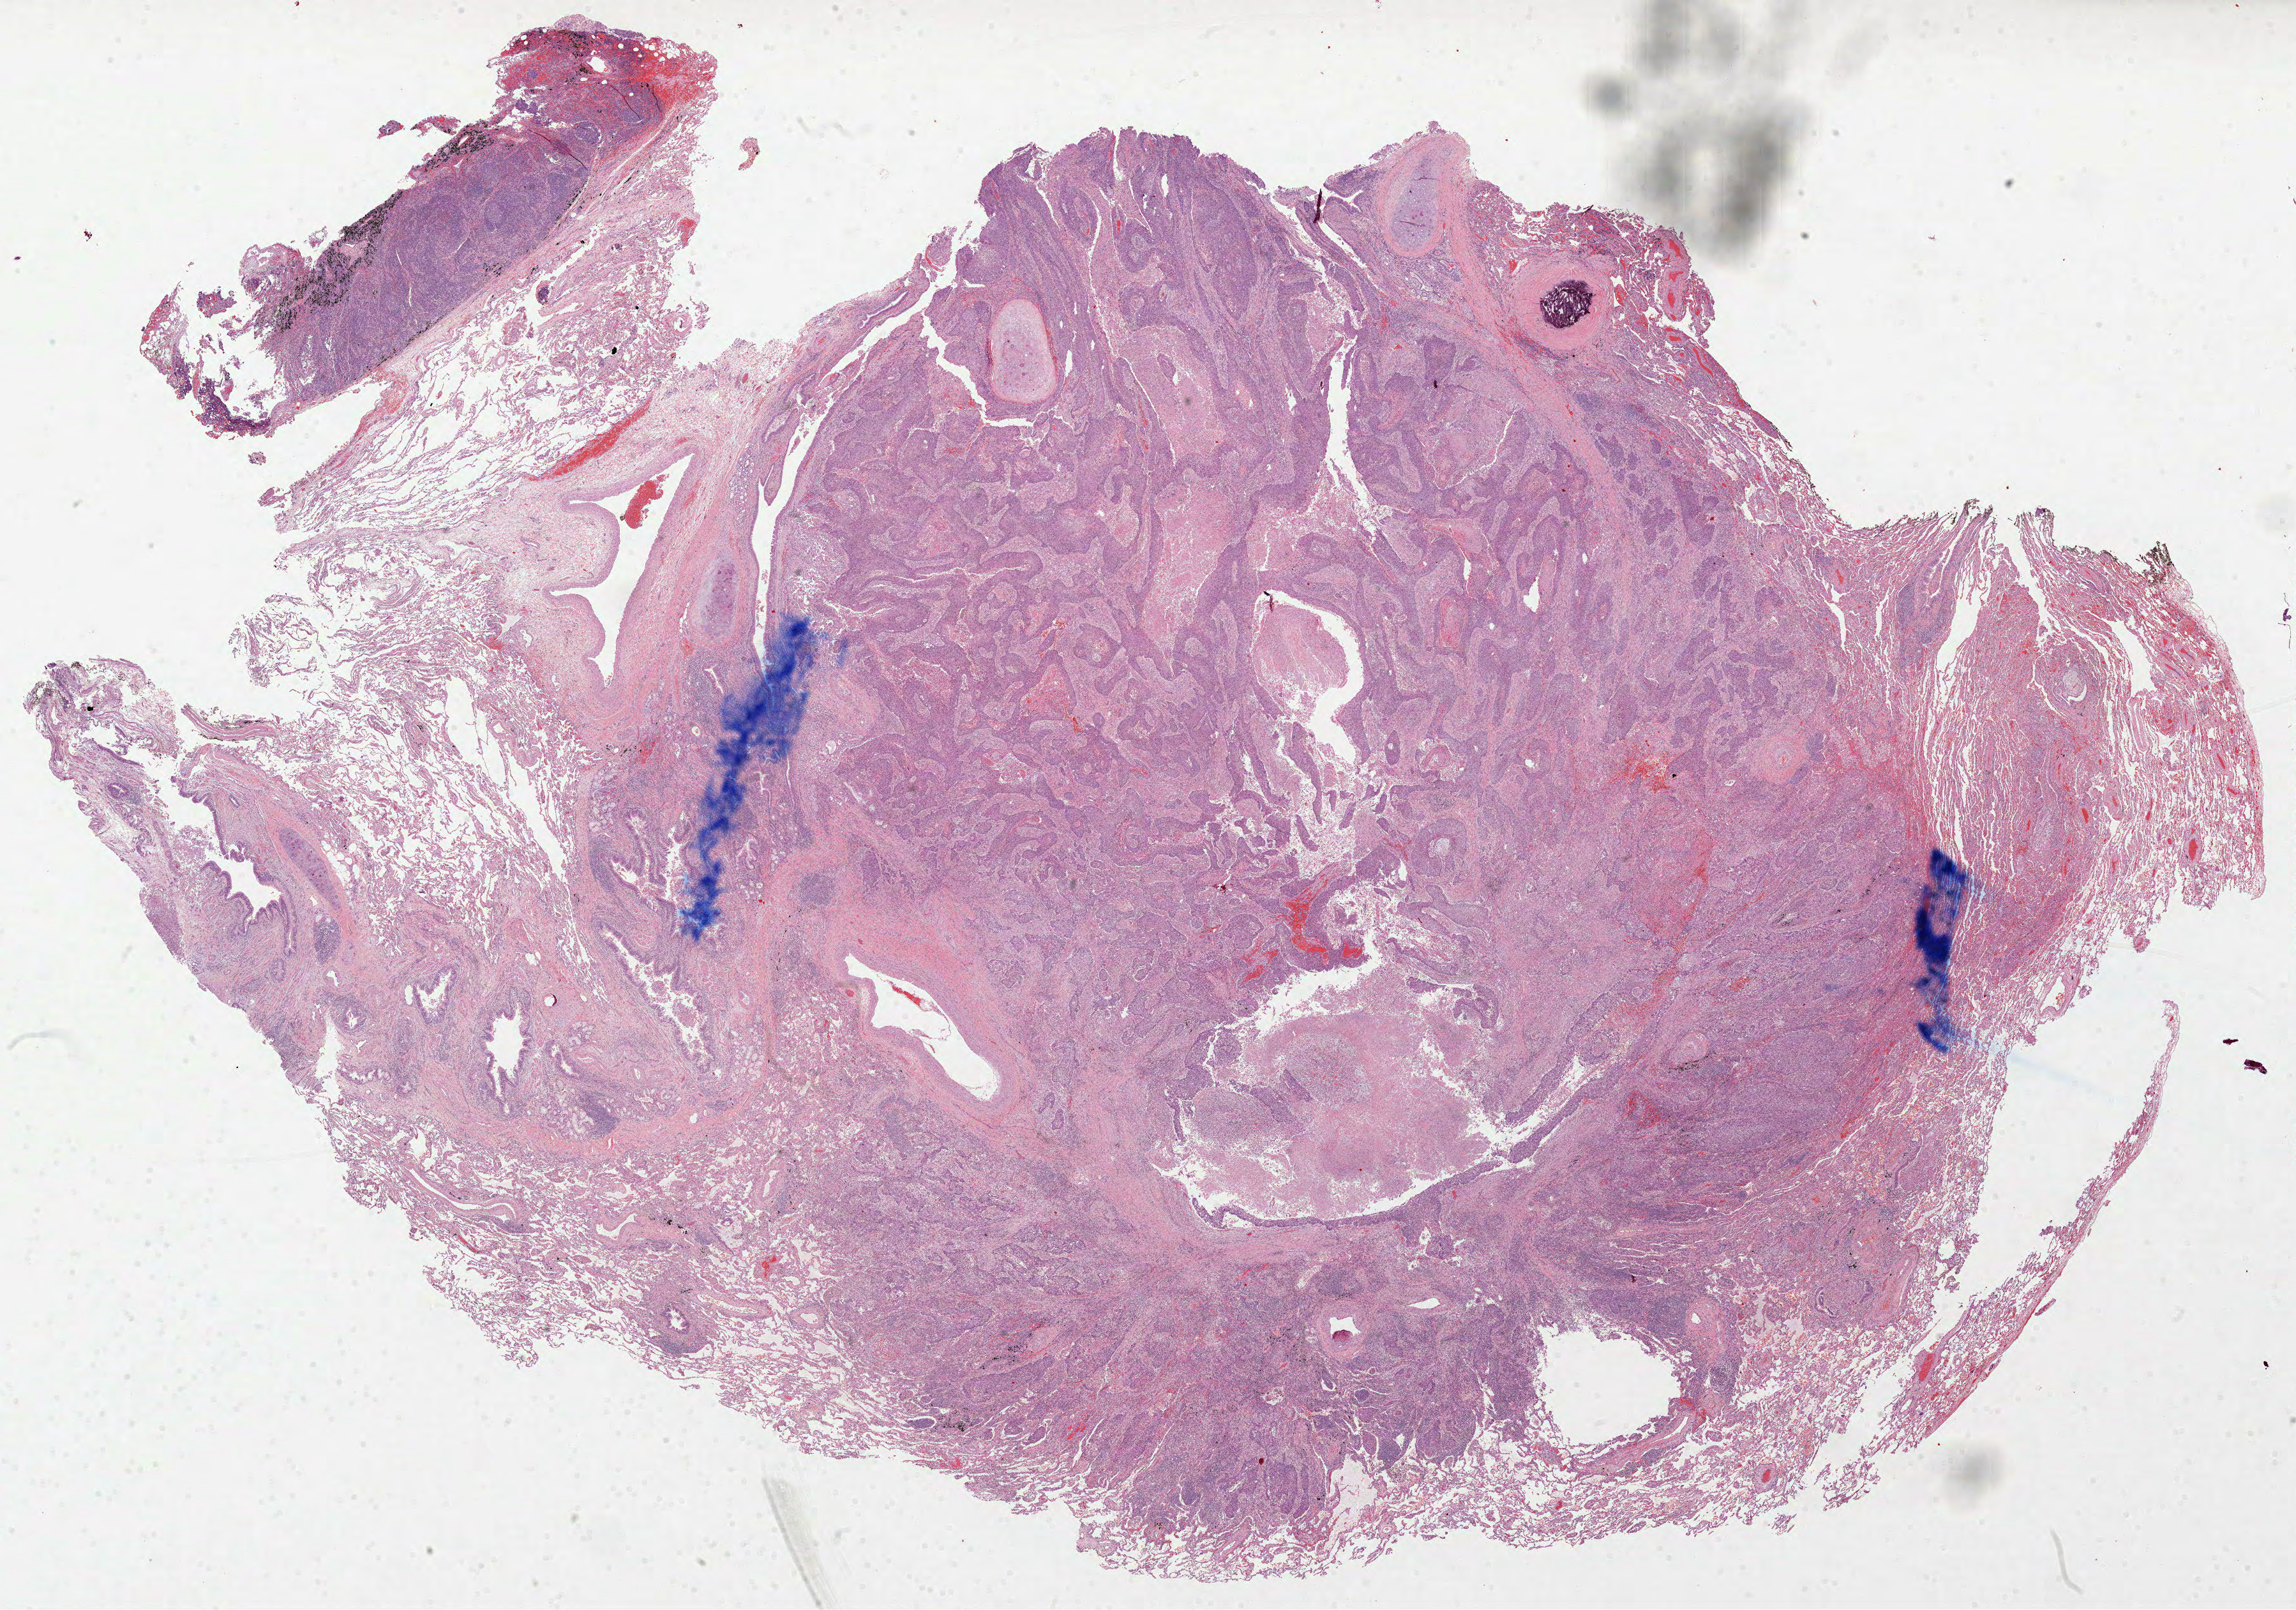
Whole-slide histology image, H&E-stained, low-resolution overview of the scanned area, about 29.0 x 20.3 mm (slide scanned at 40x), formalin-fixed paraffin-embedded (FFPE) diagnostic section, sample: primary tumour, lung. Female patient; age at initial diagnosis 62 years.
Histologic diagnosis: Squamous cell carcinoma, NOS. AJCC pathologic stage: IA.